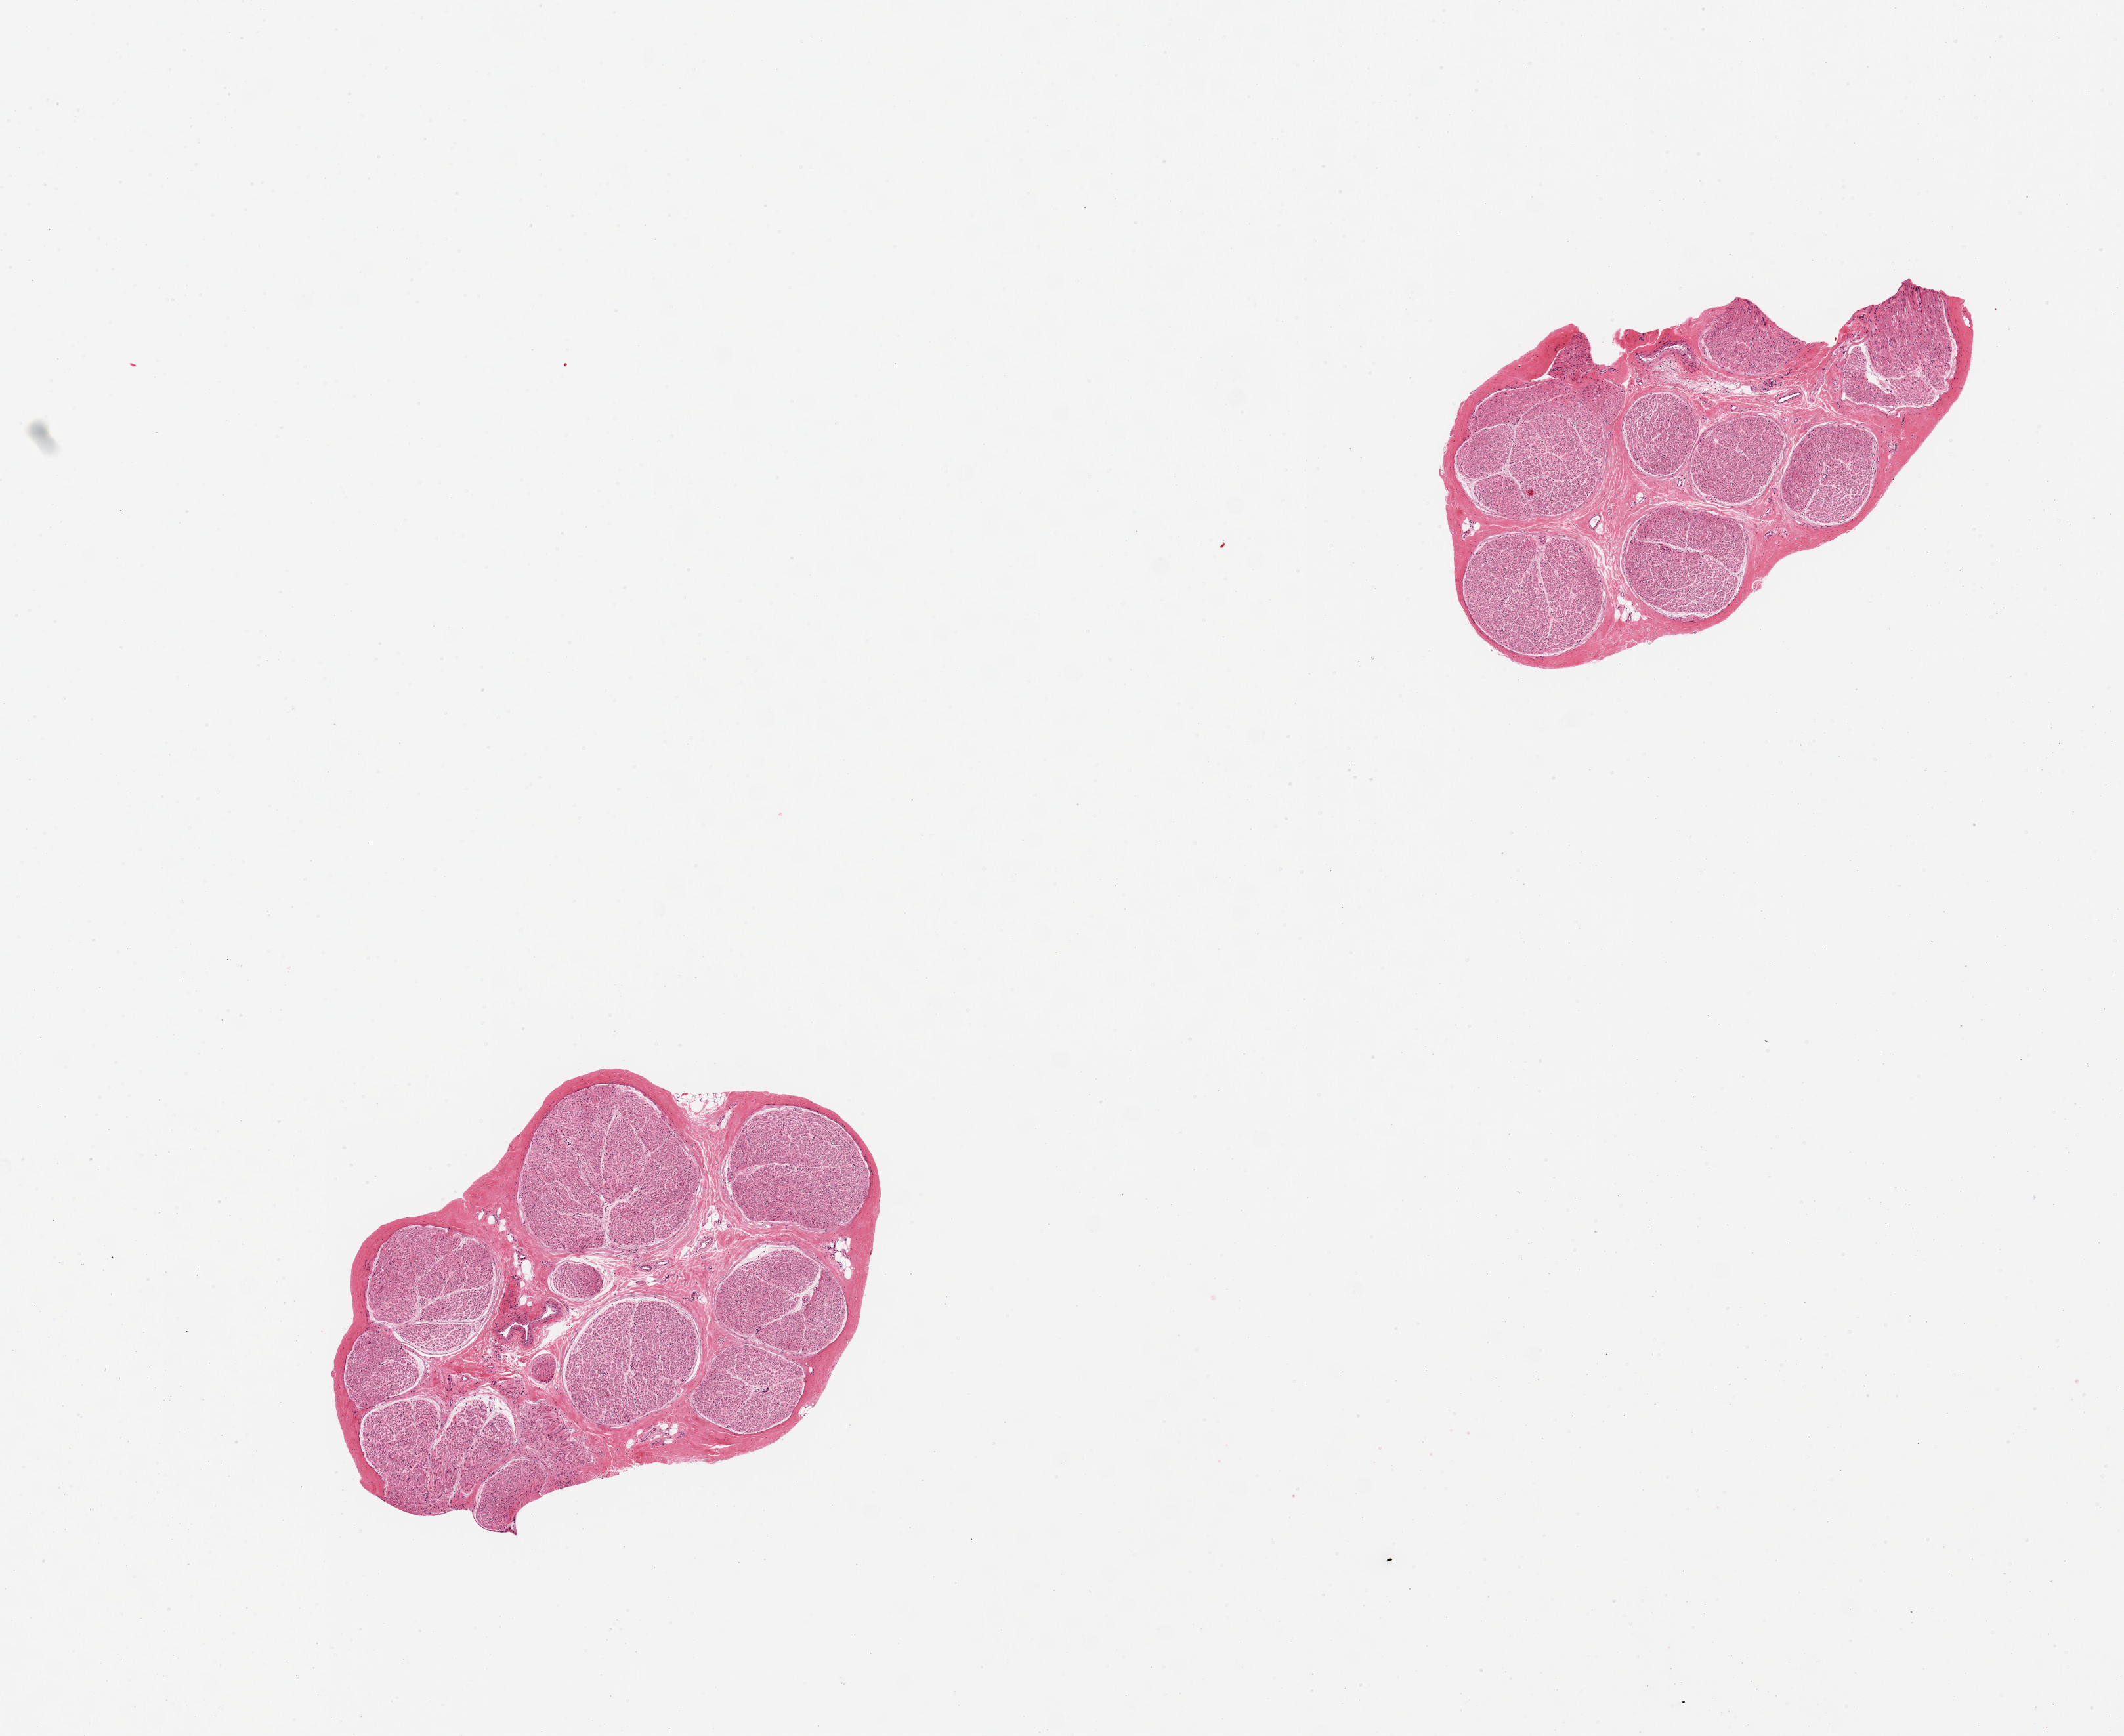
Hematoxylin and eosin (H&E) whole-slide image, brightfield, a low-resolution overview of the entire scanned area, about 12.8 x 10.5 mm (slide scanned at 20x). PAXgene-fixed paraffin-embedded (PFPE) section. Section of tibial nerve (target tissue). Tissue donor sample. Female donor.
Reviewer comment on this tissue sample: 2 pieces, clean specimens.